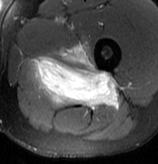
MRI of an extremity soft-tissue mass, one axial slice; slice 52 of 70 in the series (ordered by position); T2-weighted fat-saturated; MR volume resampled by the dataset authors to the PET/CT grid (not the native acquisition matrix); 3.27 mm slice thickness; 158 × 164 image matrix, field of view 154 × 160 mm. Male patient. Case-level facts recorded for this patient, not image findings: histological type: extraskeletal osteosarcoma; grade: high; site of the primary tumour: left adductur.
Outlined on this slice (expert contour drawn on MRI and transferred to this co-registered scan by the dataset authors):
- gross tumour volume (mass): bounding box [x1, y1, x2, y2] px = [29, 43, 119, 109]